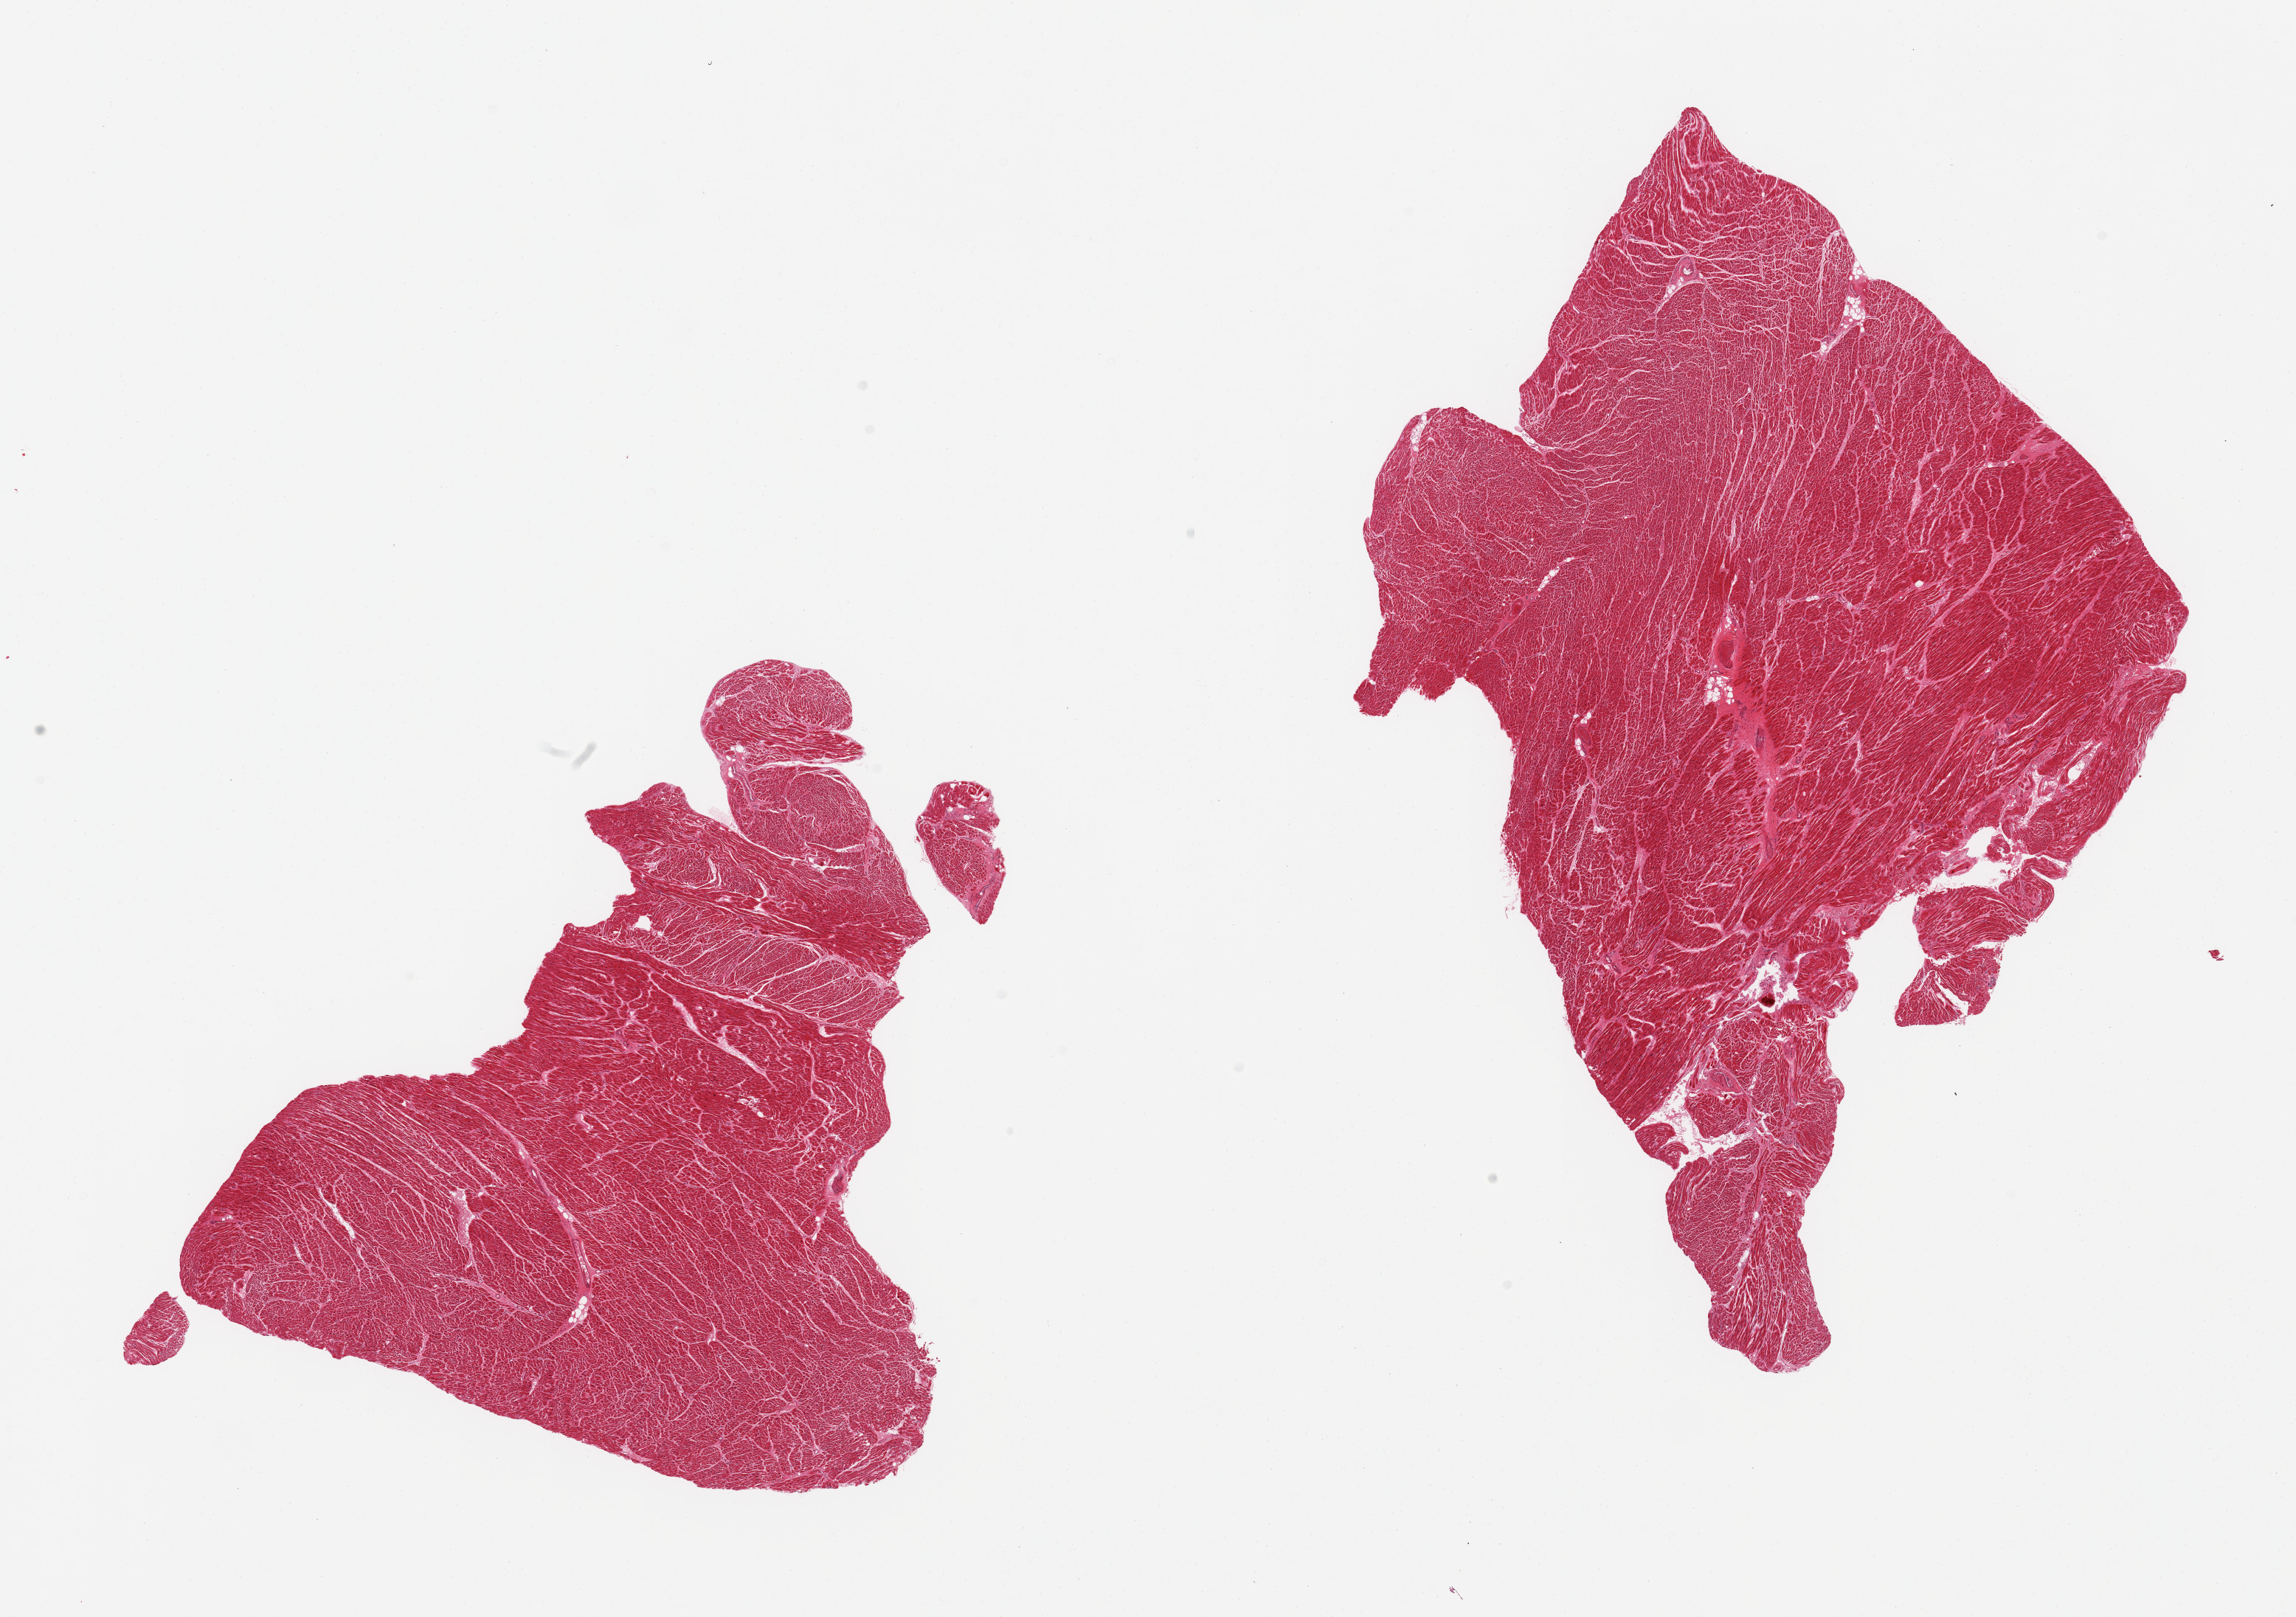
H&E whole-slide image, brightfield, shown as a low-resolution overview of the whole scanned area (about 24.6 x 17.3 mm, acquisition: 20x scan). PAXgene-fixed, paraffin-embedded tissue. Sampled site (target tissue): heart. Tissue donor sample. Female donor.
Reviewer comment on this tissue sample: 2 pieces, minimal atherosis; contraction band necrosis noted.